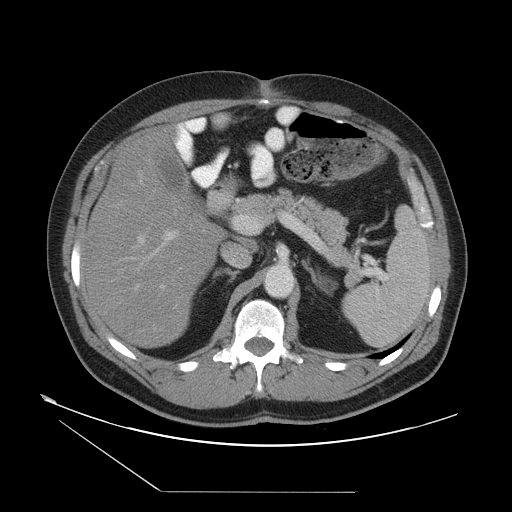
Contrast-enhanced abdominal CT, one axial slice. Reconstruction kernel STANDARD. 120 kVp. Intravenous contrast given. Soft-tissue window (W 400 / L 40 HU). 5 mm slice thickness. 512 × 512 image matrix, field of view 454 × 454 mm. Male patient, age 59 years. Case-level facts recorded for this patient, not image findings: diagnosis: colorectal cancer liver metastases, imaged before liver resection; multiple liver metastases: yes; largest metastasis: 0.3 cm; disease in both lobes: yes.
Structures marked on this image (outlined manually by an expert reader):
- hepatic veins: bounding box (x1, y1, x2, y2) in pixels: (132, 210, 176, 330)
- liver: (86, 132, 219, 348)
- planned liver remnant (the part of the liver to remain after resection): (86, 138, 219, 348)
- portal vein (with intrahepatic branches): (138, 231, 178, 290)